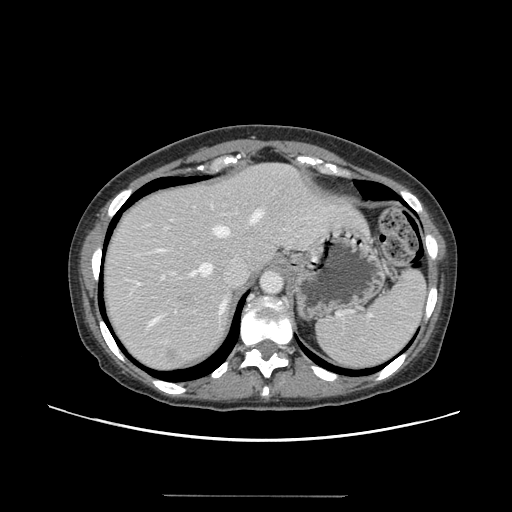
Contrast-enhanced abdominal CT, one axial slice. Slice 114 of 144 in the series (ordered by position). Intravenous contrast given. Soft-tissue window (W 400 / L 40 HU). 2.5 mm slice thickness. 512 × 512 image matrix. Female patient, age 53 years. Case-level facts recorded for this patient, not image findings: diagnosis: colorectal cancer liver metastases, imaged before liver resection; multiple liver metastases: yes; largest metastasis: 1.1 cm.
Structures marked on this image (expert manual segmentation):
- hepatic veins: bounding box (x1, y1, x2, y2) in pixels: (137, 210, 262, 325)
- liver: (104, 164, 360, 370)
- planned liver remnant (the part of the liver to remain after resection): (103, 164, 291, 300)
- portal vein (with intrahepatic branches): (161, 220, 176, 280)
- liver metastasis: (179, 294, 195, 303)
- liver metastasis: (165, 351, 178, 363)